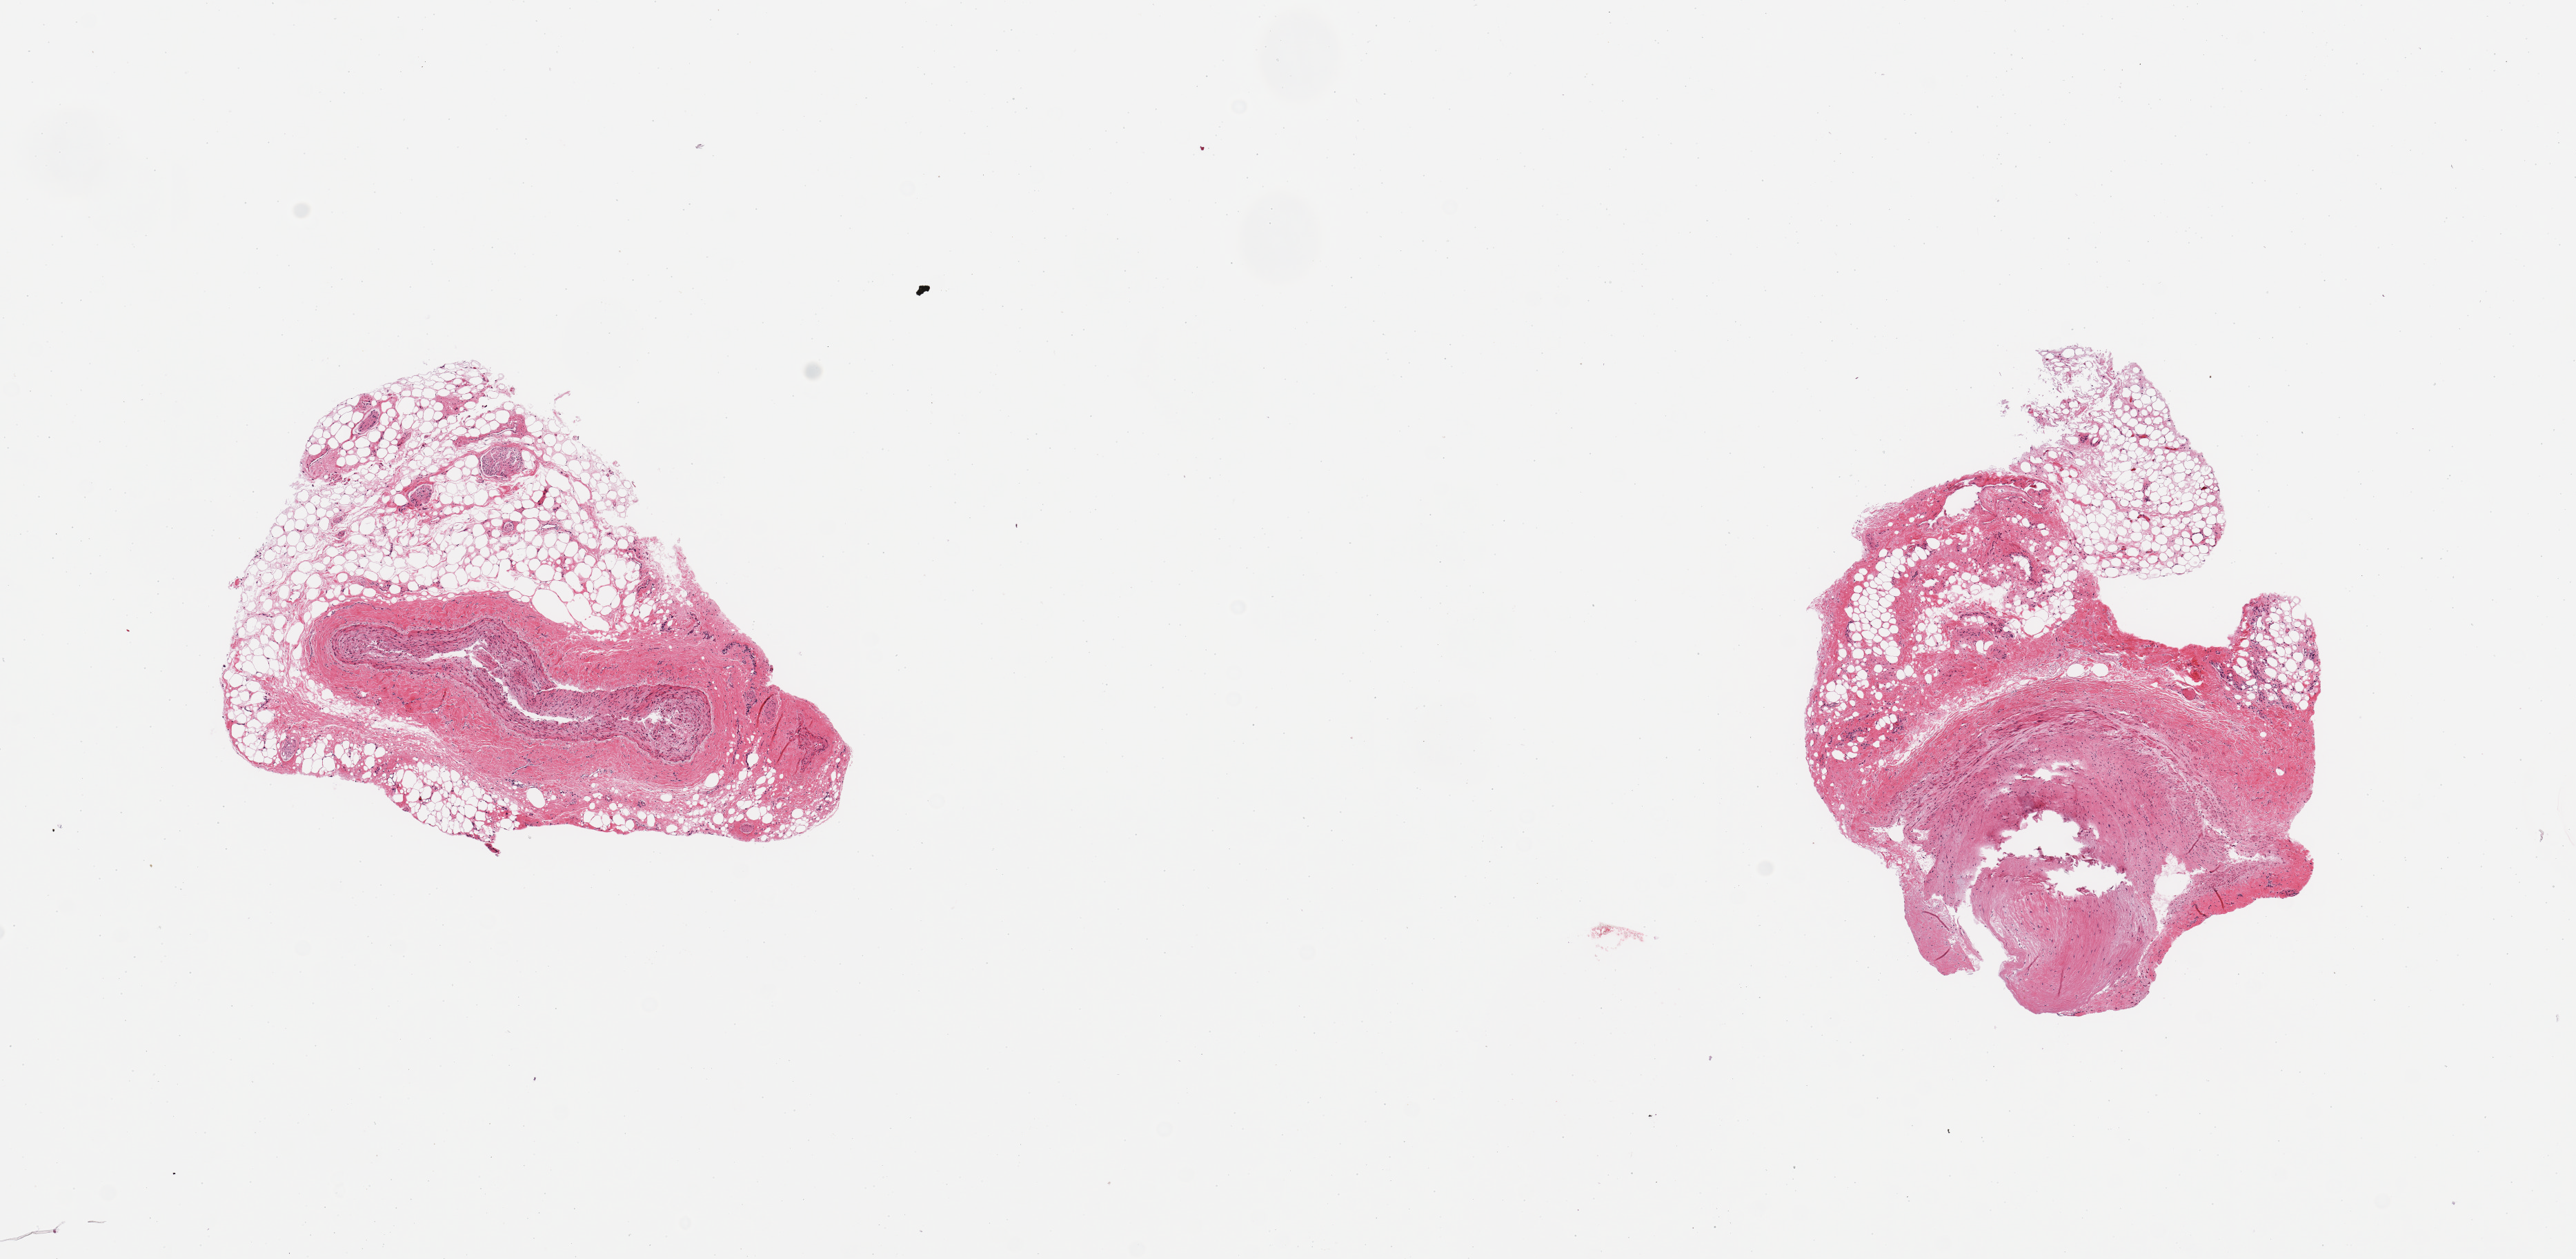
Whole-slide image, H&E stain, shown as a low-resolution overview of the whole scanned area (about 14.8 x 7.2 mm, from a 20x scan), PAXgene-fixed, paraffin-embedded tissue, sampled site (target tissue): coronary artery, tissue donor sample. Donor sex: male.
Reviewer comment on this tissue sample: 2 pieces, more than 60% adherent fat/fibrous tissue, apparent twig, not branch of left main coronary artery.